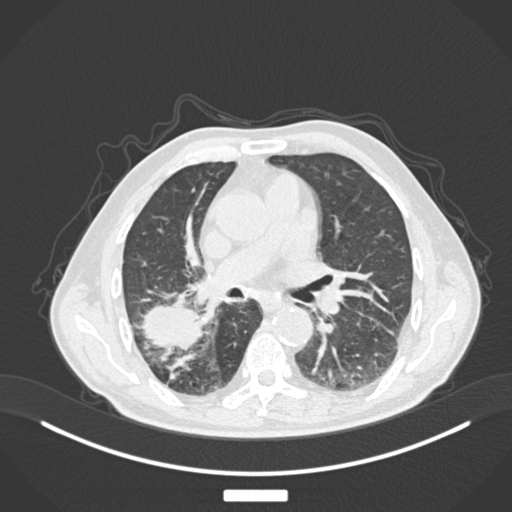
Chest CT, one axial slice. Slice 93 of 201 in the series (ordered by position). Reconstruction kernel B30f. 120 kVp. Lung window (W 1500 / L -600 HU). 1 mm slice thickness. 512 × 512 image matrix, field of view 400 × 400 mm. Patient: male, 72 years. Case-level facts recorded for this patient, not image findings: clinical TNM (as recorded): T3 N2 M0.
Outlined on this slice (bounding box drawn by a radiologist):
- lung tumour (recorded histology: adenocarcinoma): bounding box (x1, y1, x2, y2) in pixels: (140, 296, 205, 354)